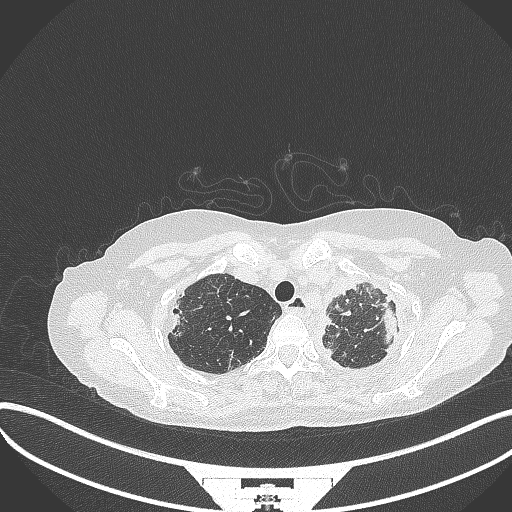
Chest CT, one axial slice; slice 291 of 373 in the series (ordered by position); 120 kVp; lung window (W 1500 / L -600 HU); 1 mm slice thickness; 512 × 512 image matrix, field of view 400 × 400 mm. Patient: female, 56 years. Case-level facts recorded for this patient, not image findings: clinical TNM (as recorded): T1 N0 M0.
Structures marked on this image (bounding box drawn by a radiologist):
- lung tumour (recorded histology: adenocarcinoma): bounding box <381,303,406,348> (left, top, right, bottom; pixels)